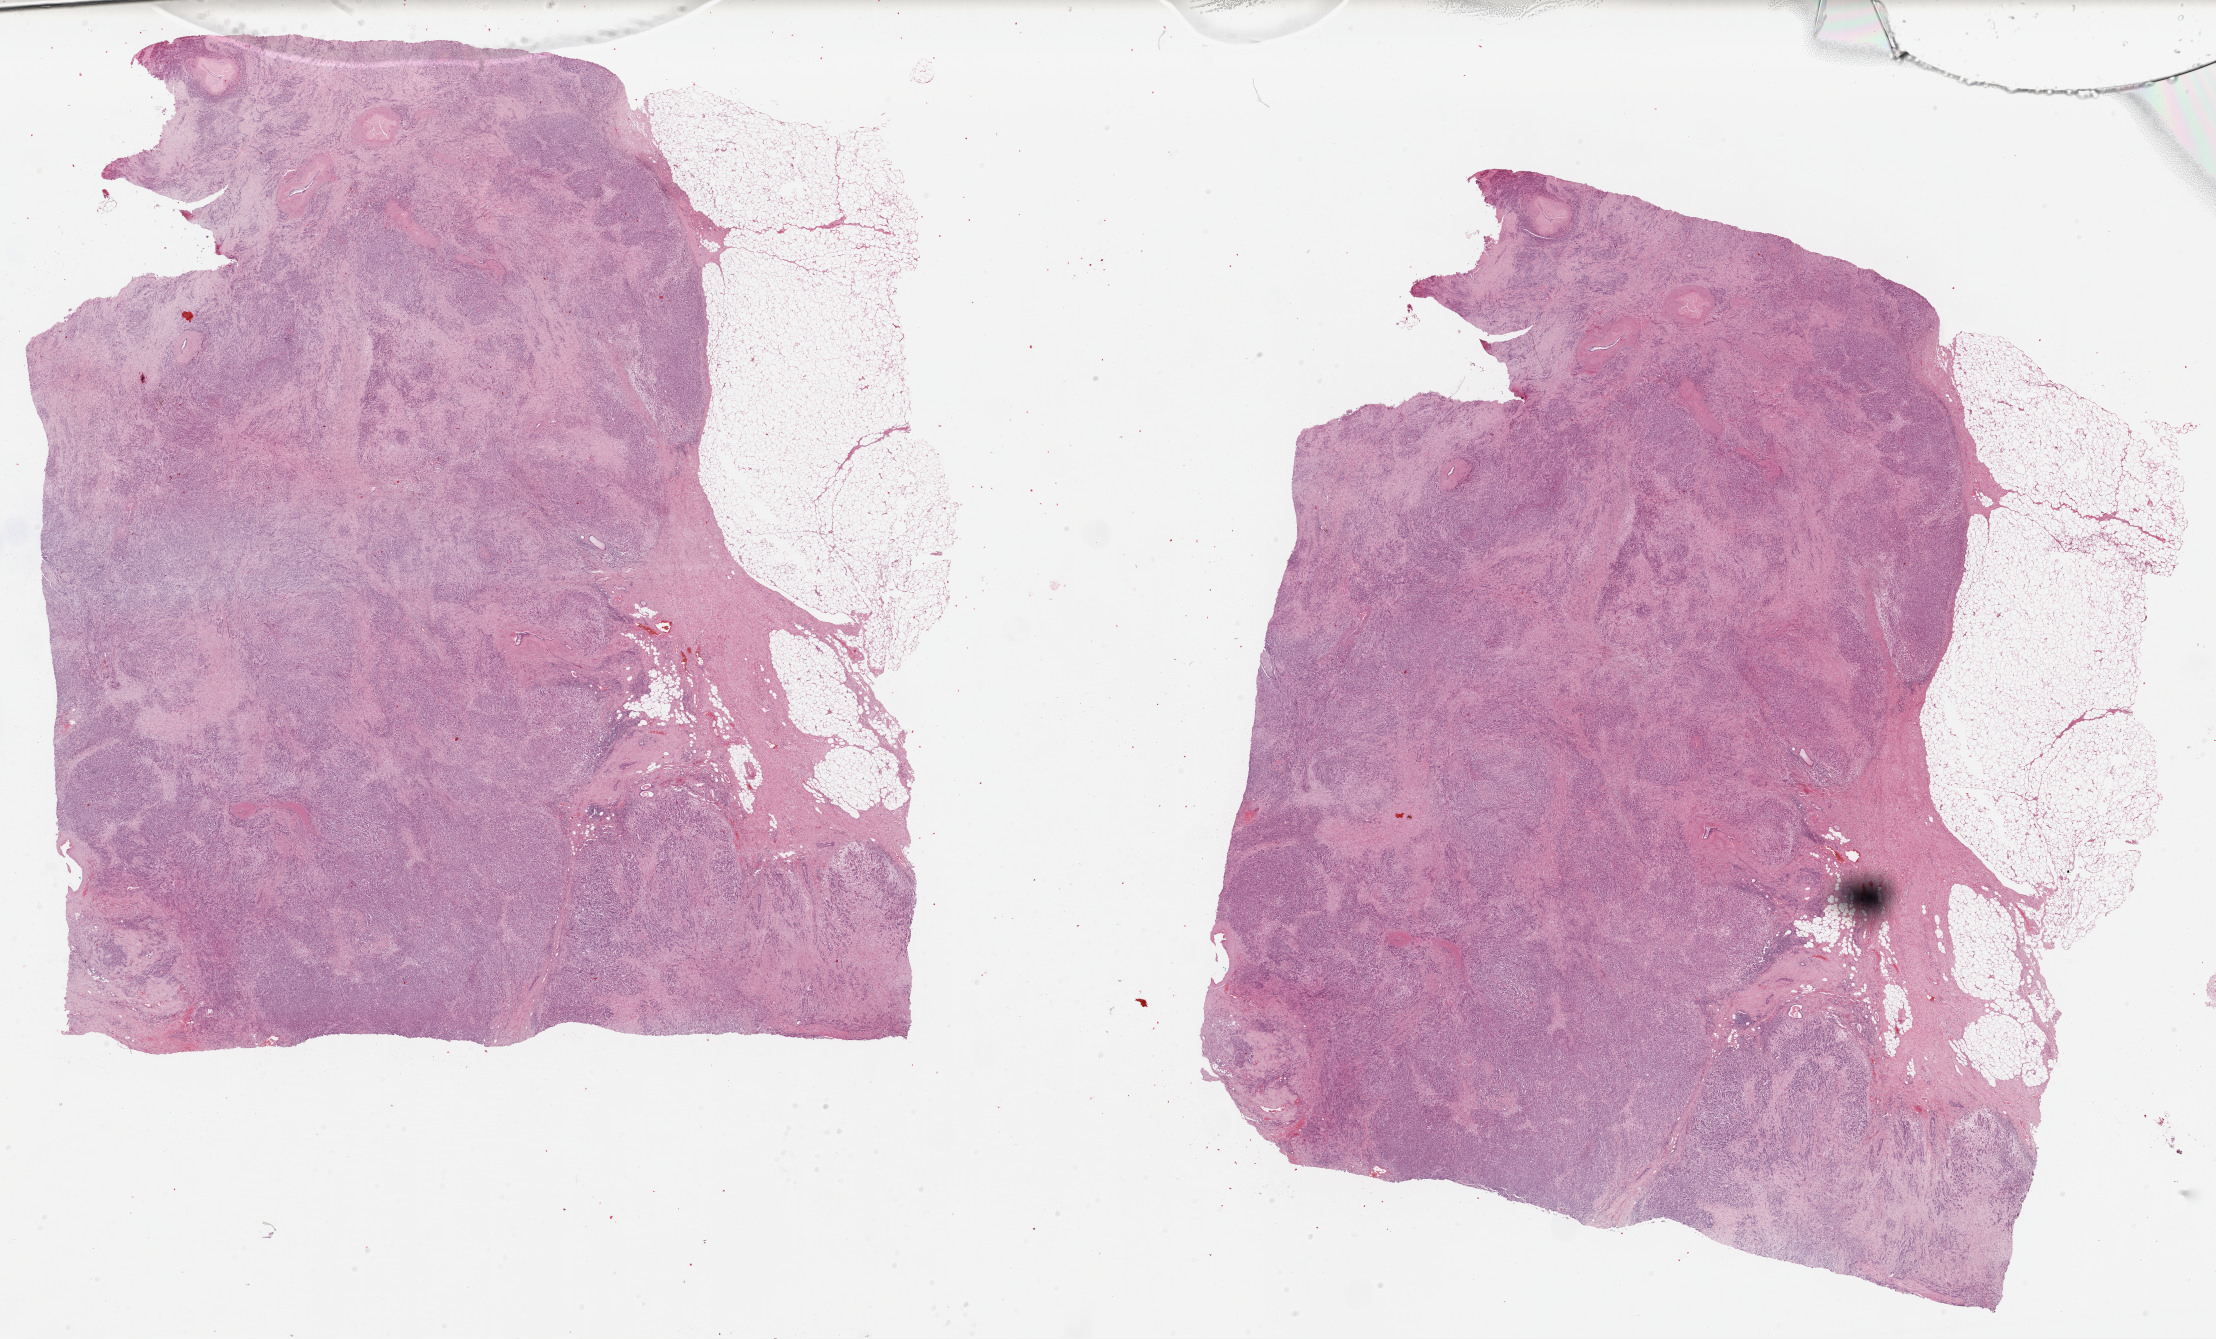
Digitized Hematoxylin and eosin (H&E) stained tissue section (whole slide), shown as a low-resolution overview of the whole scanned area (about 35.0 x 21.2 mm, slide scanned at 40x). FFPE section. Sample: primary tumour, breast. Patient: female, age at initial diagnosis 80 years.
• pathologic diagnosis: Infiltrating duct carcinoma, NOS
• lymph nodes positive (case pathology): 1 of 22 examined
• TNM: T3 N1a MX
• laterality: left
• AJCC pathologic stage: IIIA (7th edition)